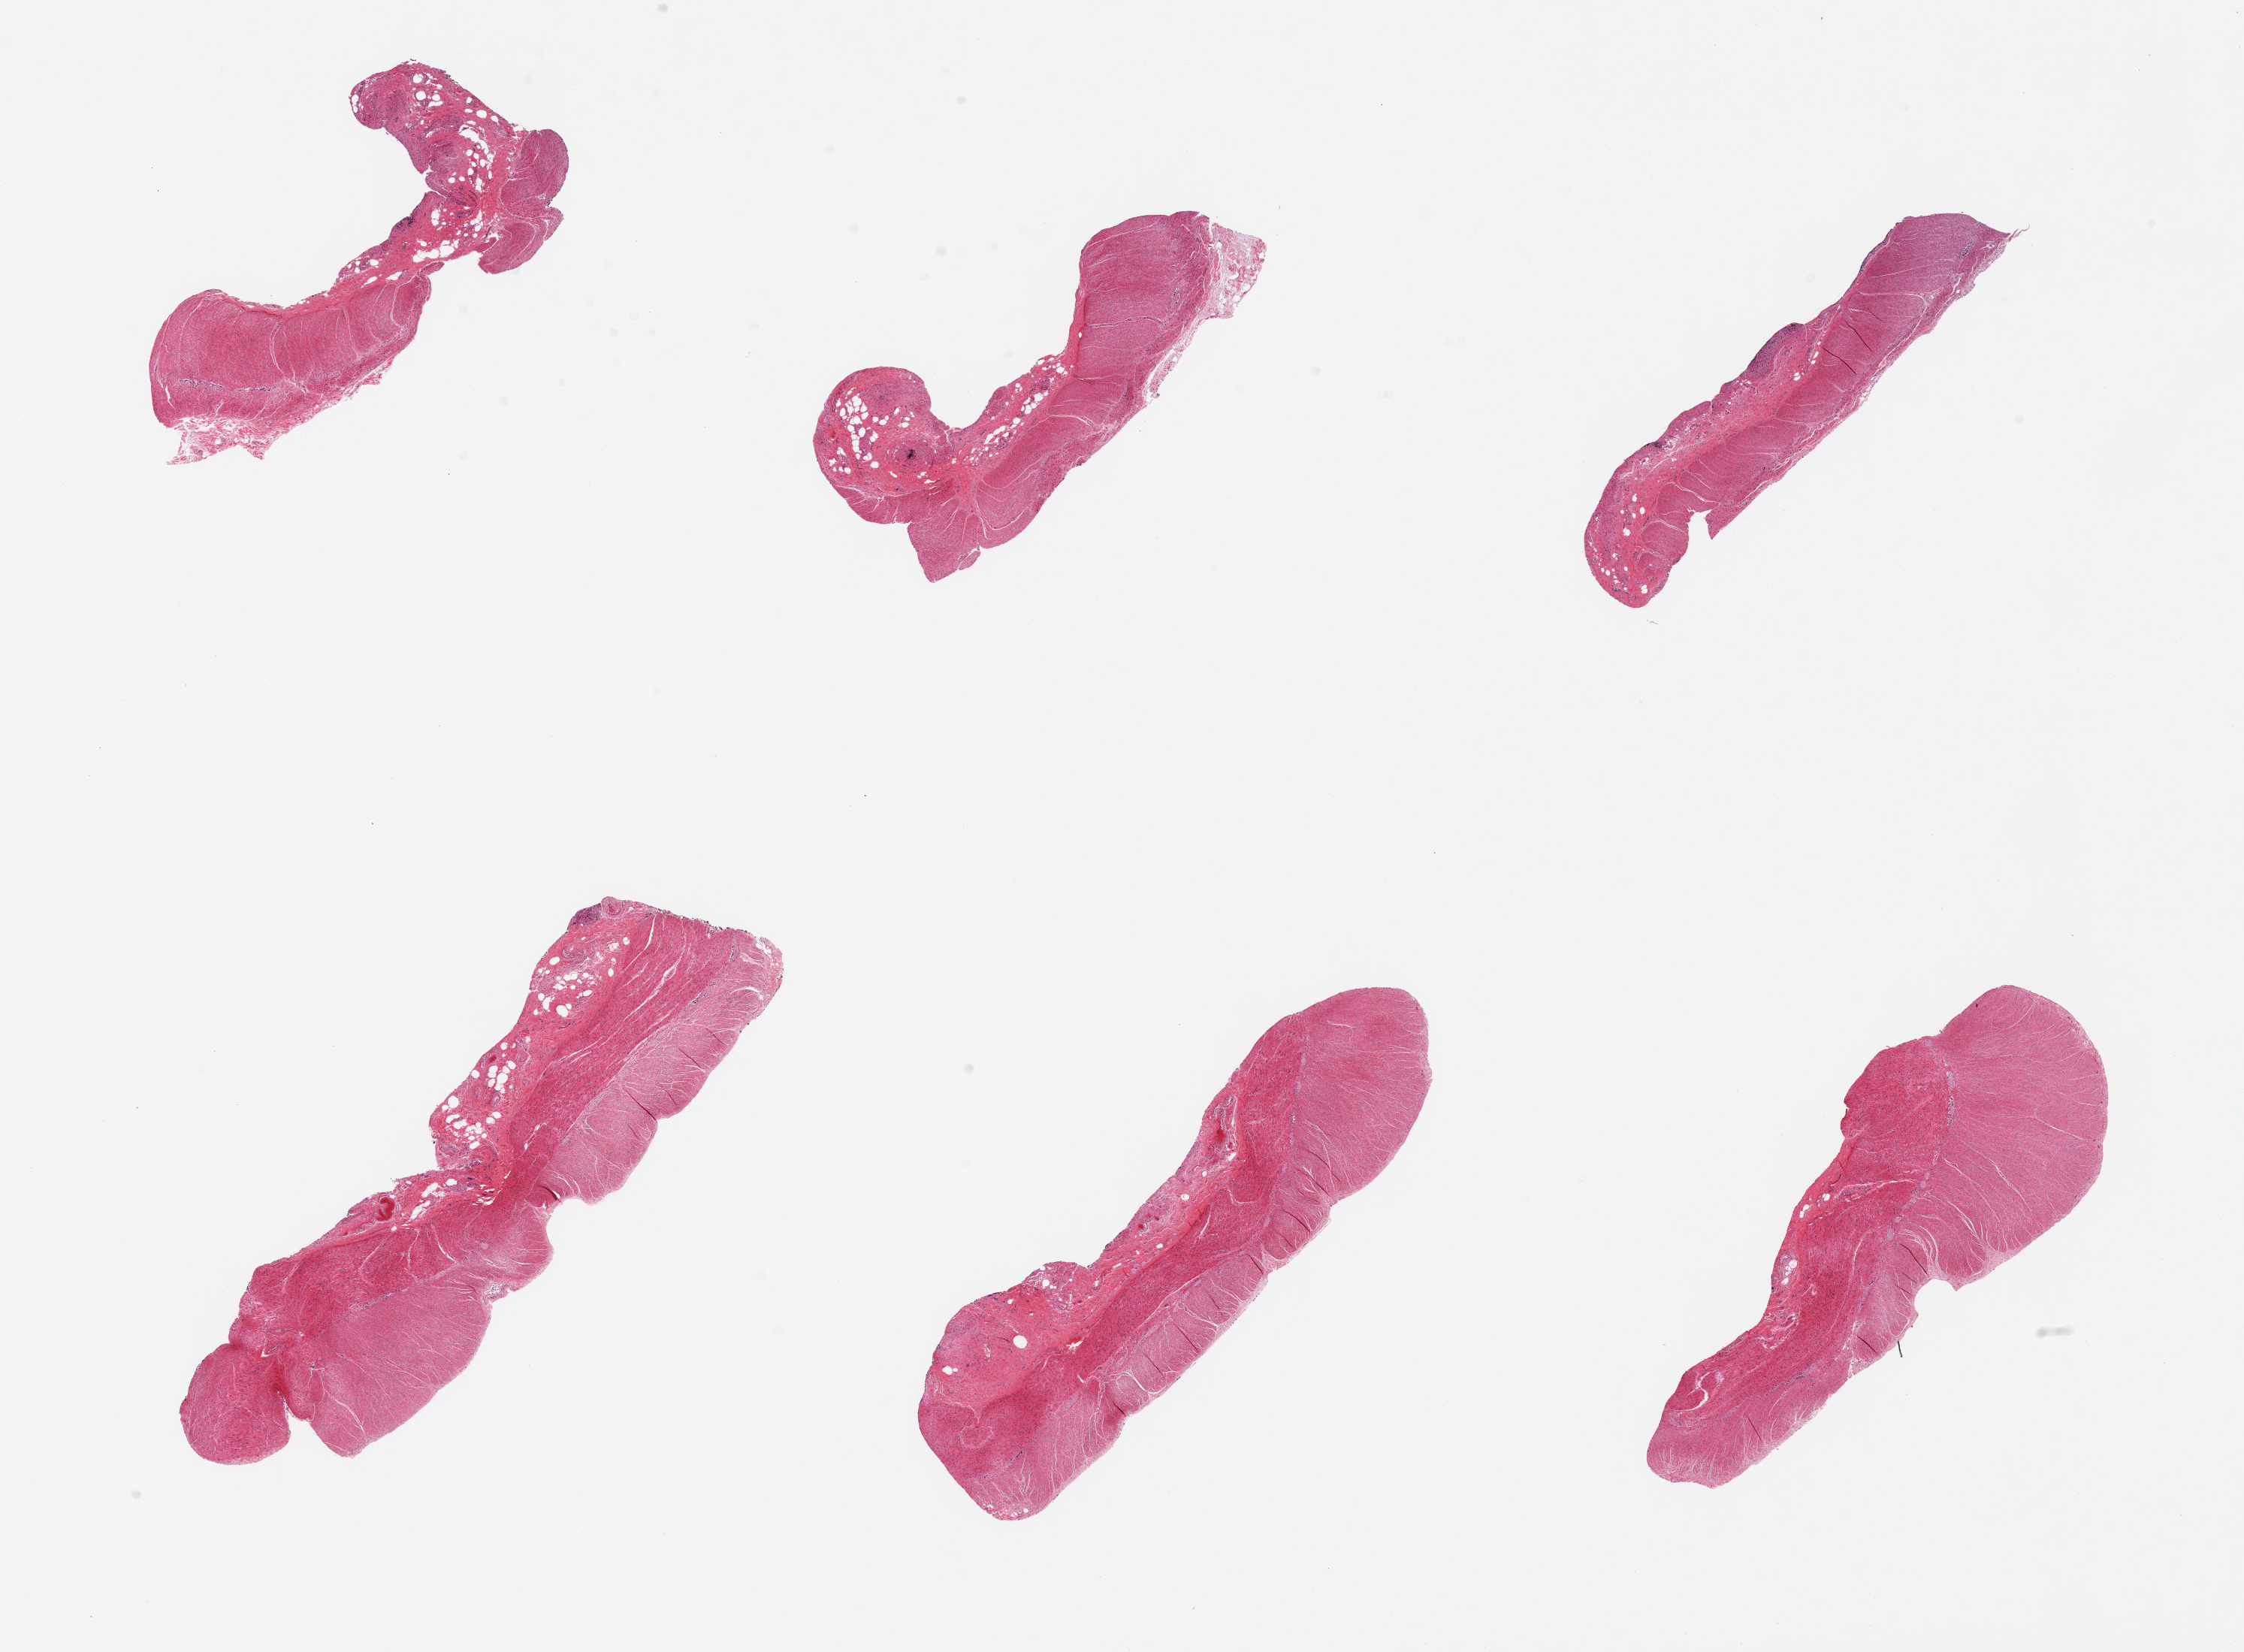
H&E whole-slide image — low-resolution overview of the scanned area, about 23.6 x 17.4 mm (slide scanned at 20x), PAXgene-fixed, paraffin-embedded tissue, sampled site (target tissue): sigmoid colon, donor tissue sample. Female donor.
- review note (as recorded): 6 pieces; up to 40% submucosal fibroadipose tissue